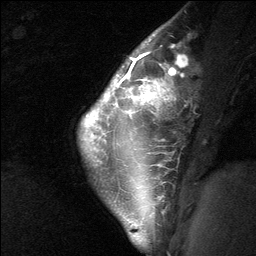
Breast MRI (dynamic contrast-enhanced), one sagittal slice; slice 49 of 64 in the series (ordered by position); dynamic contrast-enhanced study with each time point stored as its own series, time point 2 of 3 at this slice position (early post-contrast, ordered by acquisition time); 1.5 T; TE 4.8 ms, TR 27 ms; 256 × 256 image matrix, field of view 180 × 180 mm. Female patient, age 26 years. From the clinical record (not read from this slice): setting: breast cancer imaged before/during neoadjuvant chemotherapy; receptor status: HR-positive, HER2-negative.
Annotated regions visible in this slice (semi-automatic segmentation, software-assisted and operator-edited):
- analysis volume of interest (the breast-tissue region the enhancement analysis was run in; not a lesion): bounding box (x1, y1, x2, y2) in pixels: (86, 43, 181, 138)
- tumour enhancement mask (voxels above the 90 % enhancement threshold inside the analysis volume of interest): (119, 53, 175, 100)